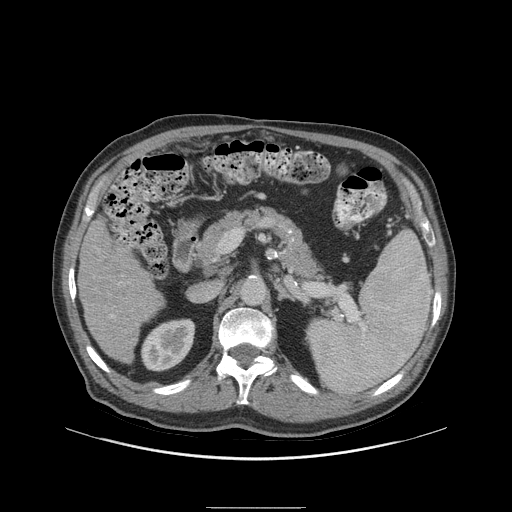
Contrast-enhanced abdominal CT (liver protocol), one axial slice; slice 44 of 105 in the series (ordered by position); soft-tissue window (W 400 / L 40 HU); 2.5 mm slice thickness; 512 × 512 image matrix. Case-level facts recorded for this patient, not image findings: diagnosis: hepatocellular carcinoma (patient treated with transarterial chemoembolisation; whether this scan precedes or follows treatment is not stated here); TNM stage (as recorded): Stage-I.
Outlined on this slice (semi-automatic segmentation, software-assisted and operator-edited):
- liver parenchyma outside the tumour (the mass and vessels are separate outlines, so this box may not span the whole liver): bounding box (x1, y1, x2, y2) in pixels: (78, 218, 162, 362)